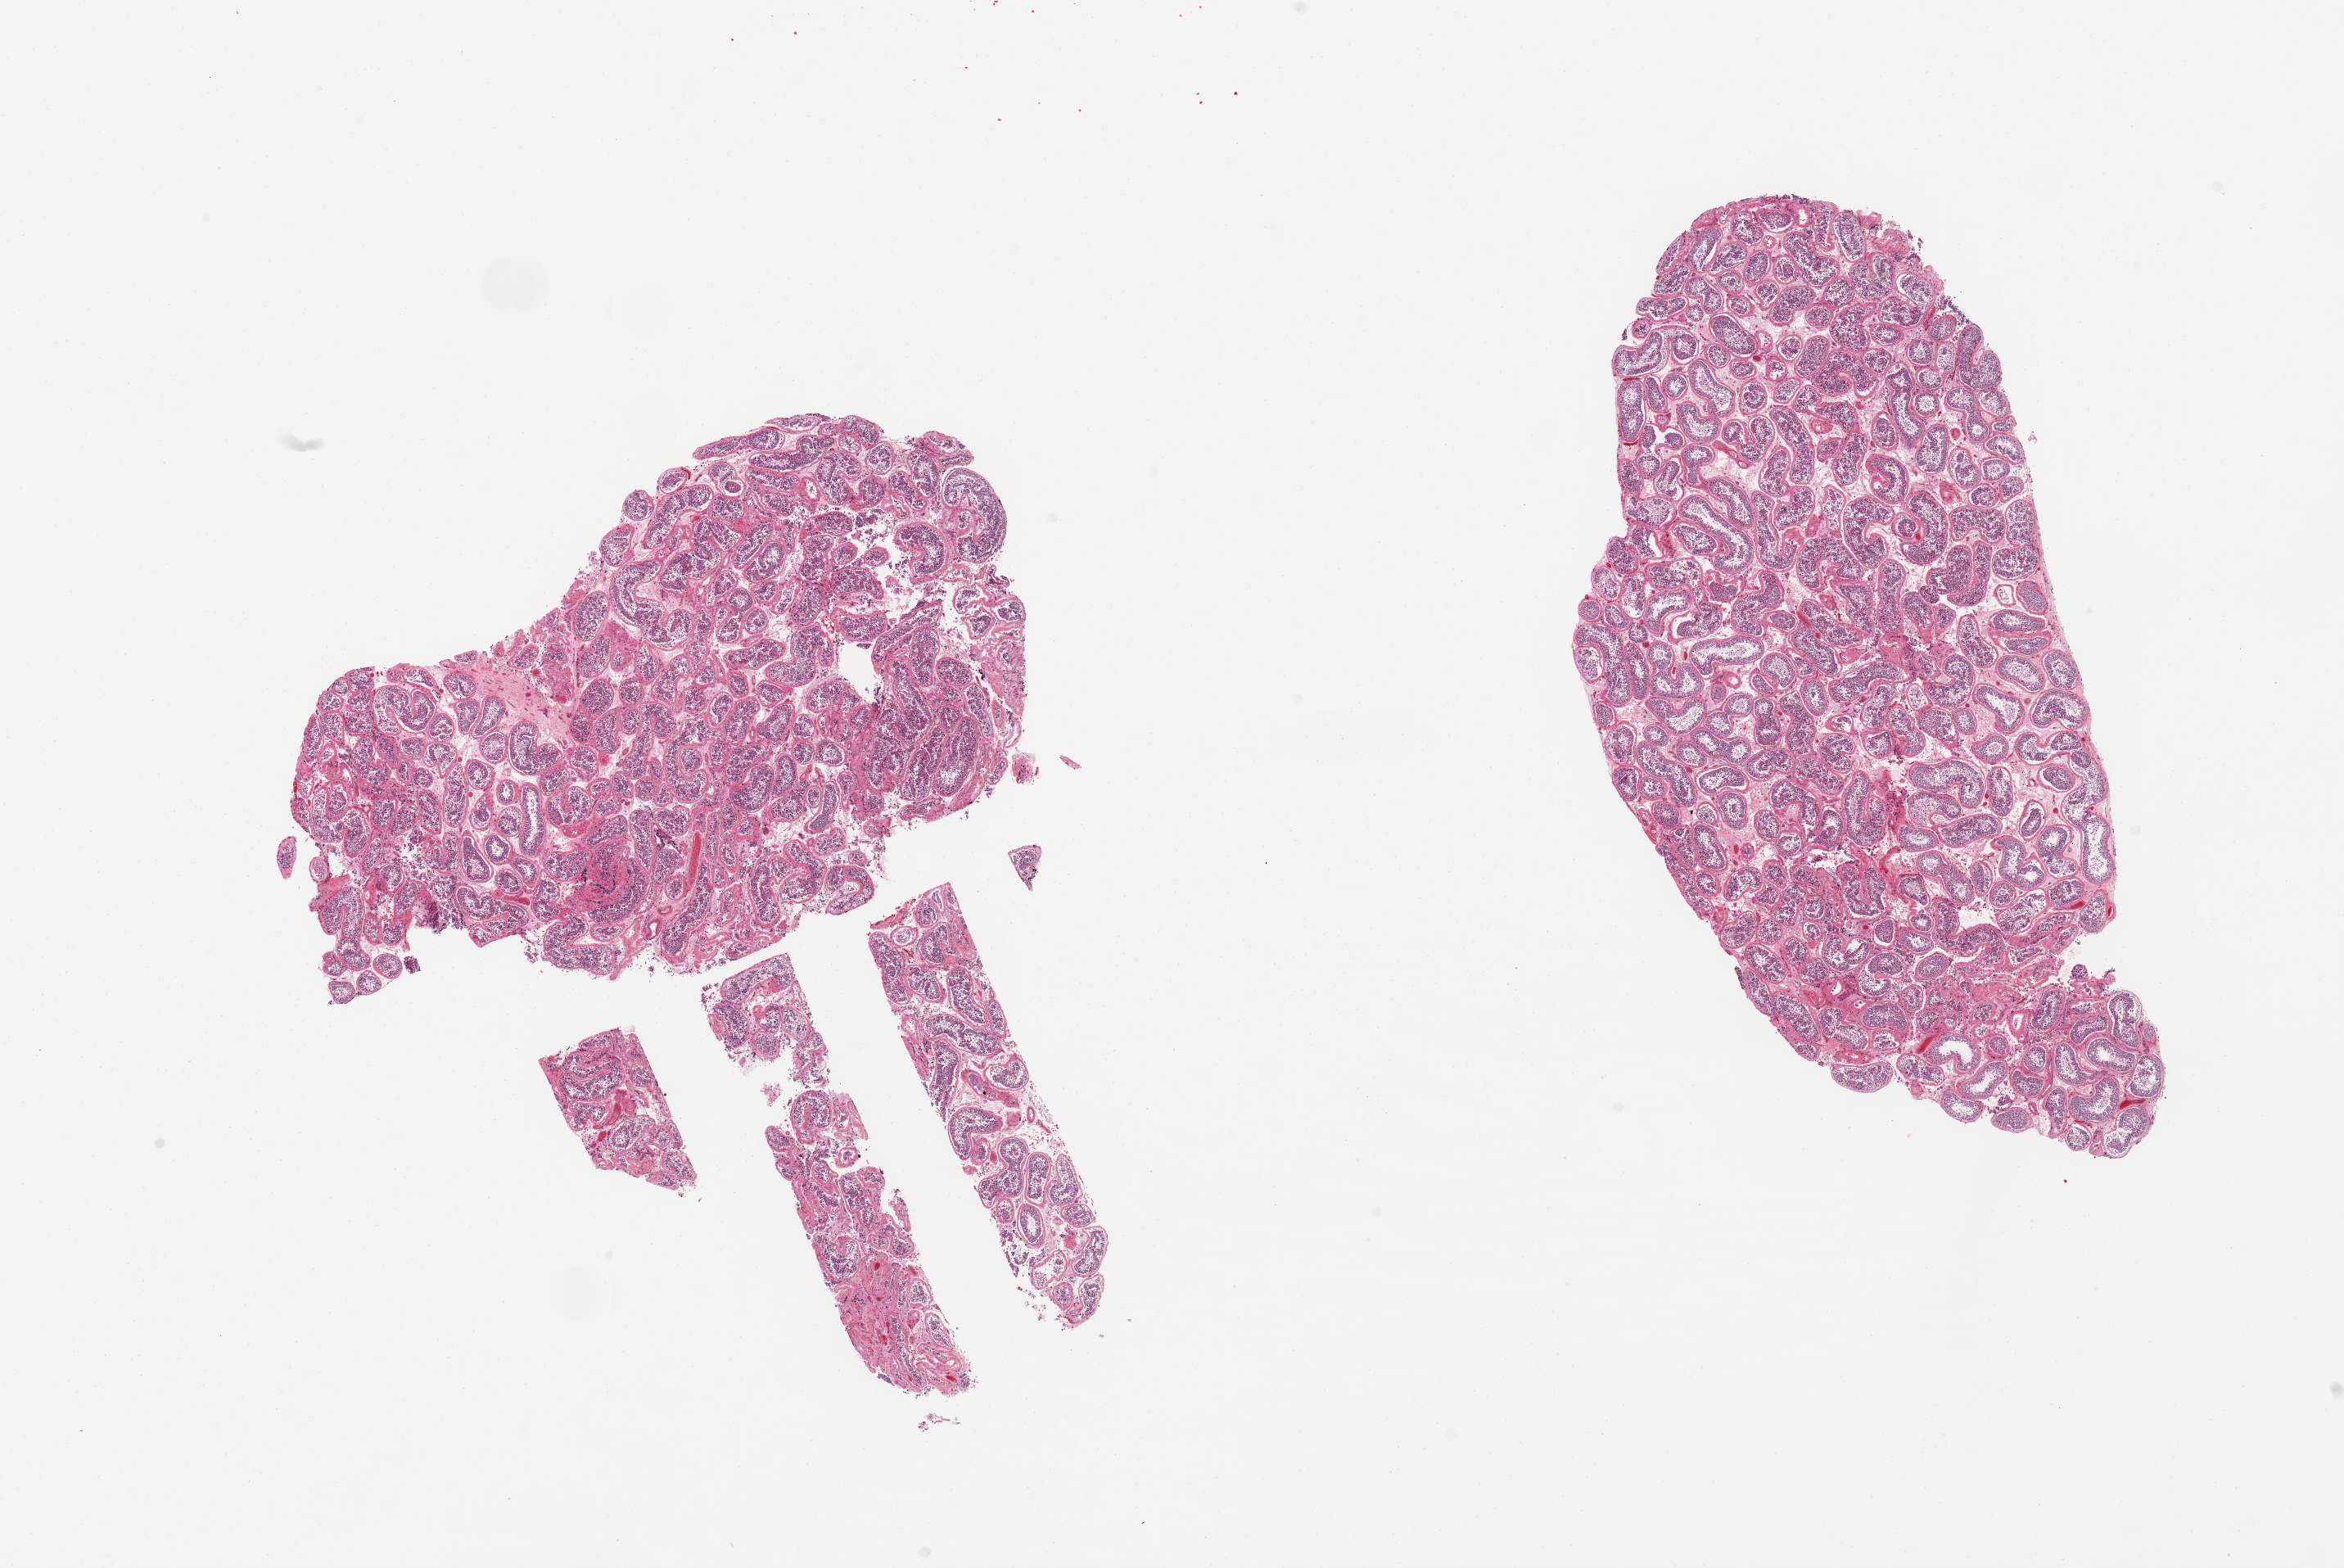
Digitized haematoxylin and eosin-stained section — low-resolution overview of the scanned area, about 22.6 x 15.1 mm; PAXgene-fixed, paraffin-embedded tissue; target tissue: testis; donor tissue sample. Donor: male.
Reviewer comment on this tissue sample: 2 pieces; spermatogenesis is present, increased peritubular fibrosis.